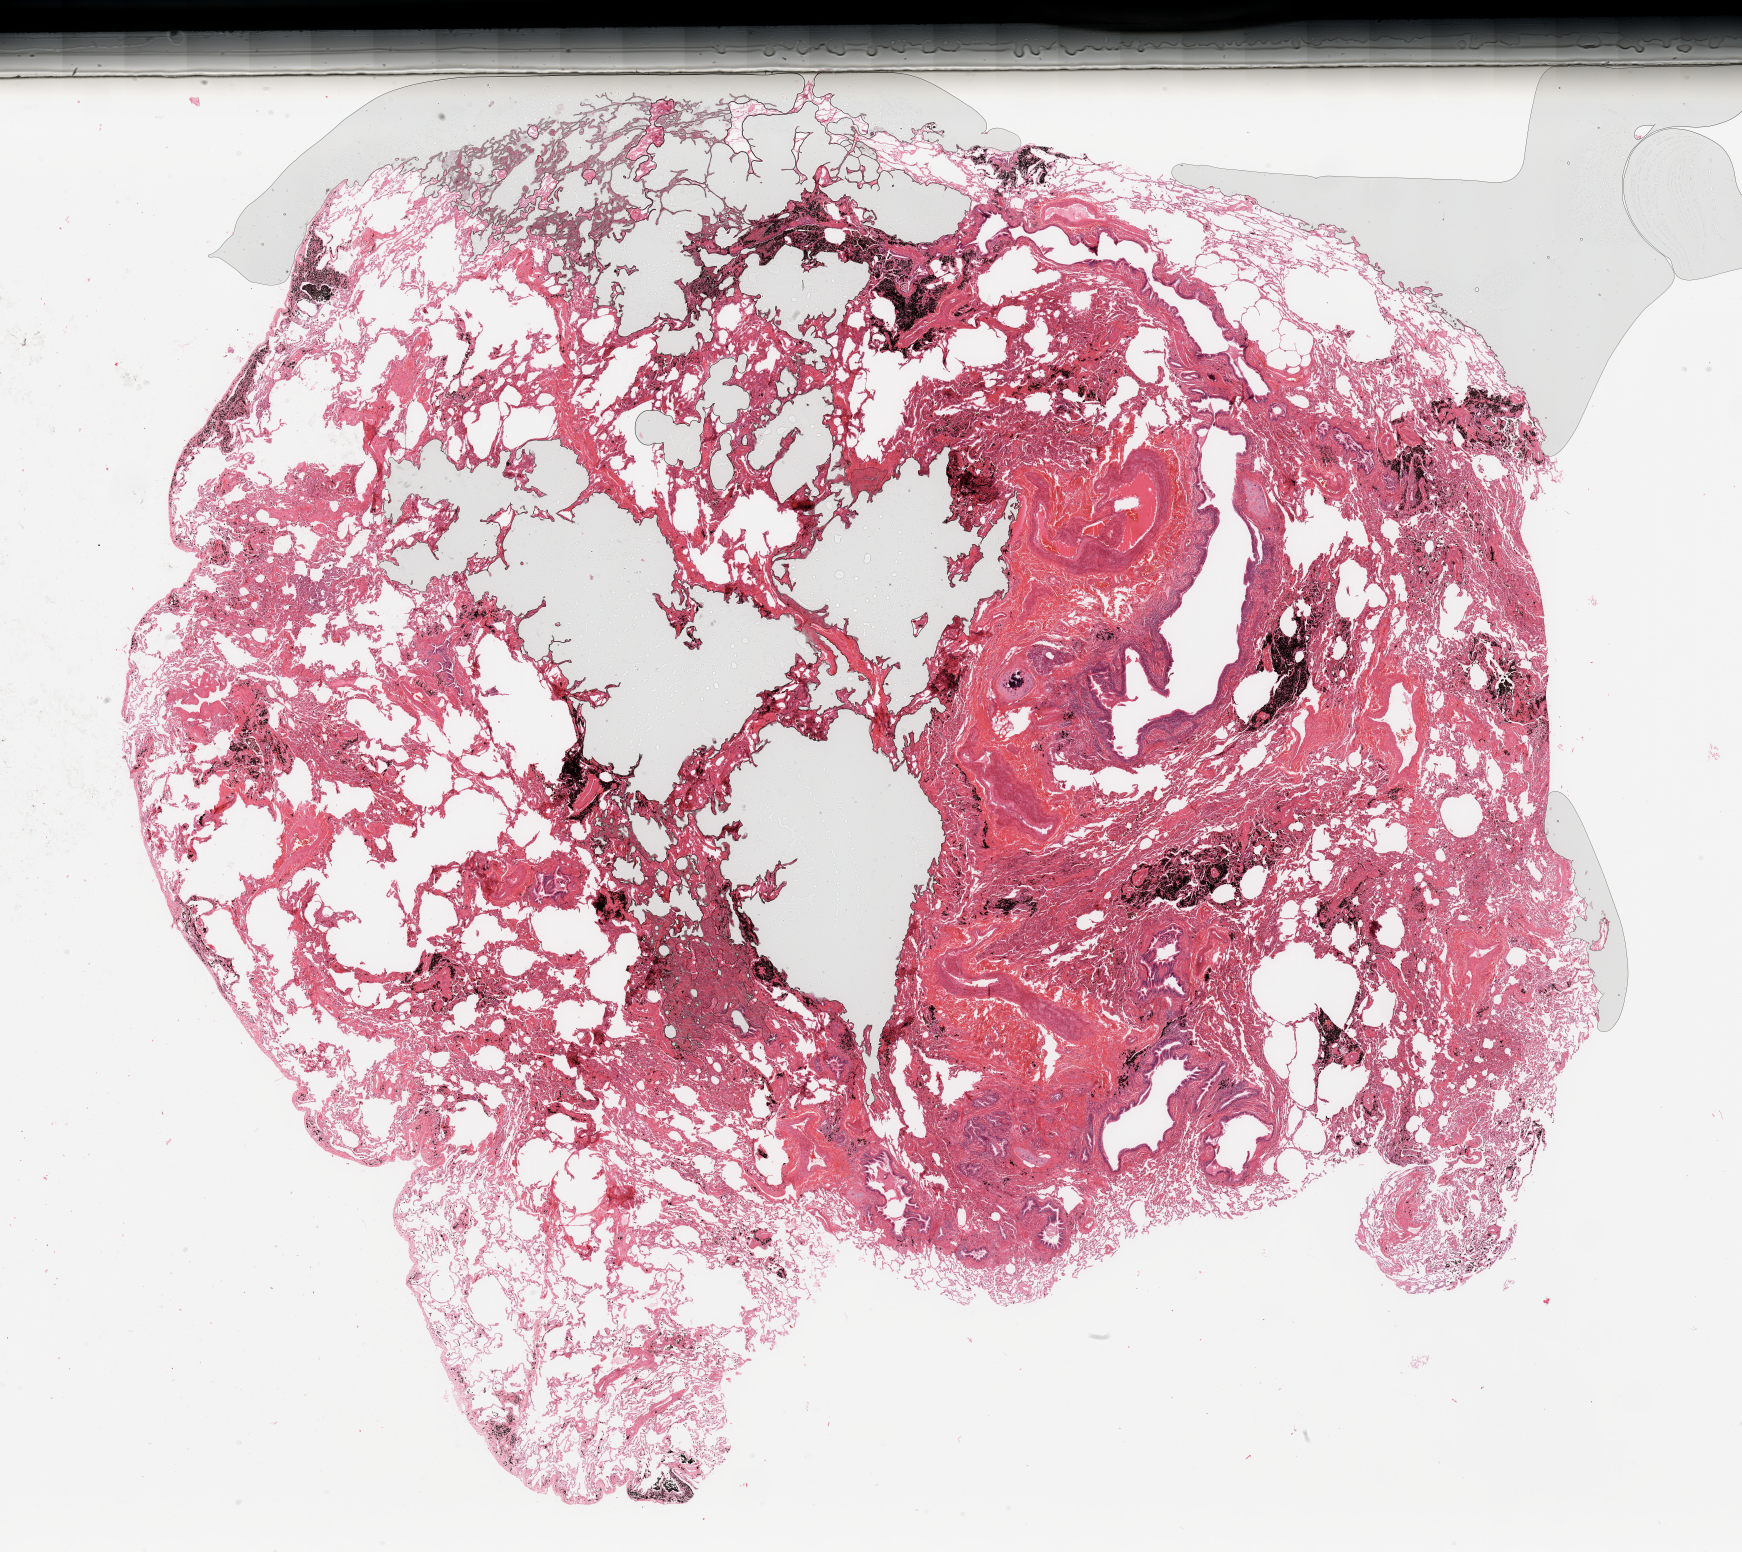
Whole-slide histology image, H&E-stained, a low-resolution overview of the entire scanned area, about 27.6 x 24.6 mm (acquisition: 20x scan); normal (non-tumour) tissue sample, lung. Patient: male, age 64 years.
This section: normal (non-tumour) tissue from the same patient. Patient diagnosis (cohort enrolment): squamous cell carcinoma (lung).